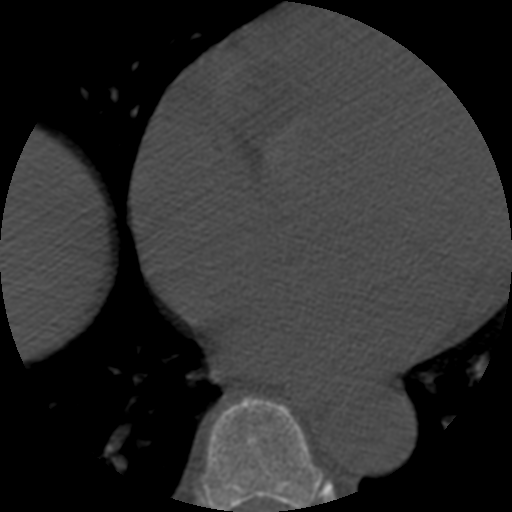
CT including the spine, one axial slice. Position 327 of 508 along the scan axis. Bone window (W 1800 / L 400 HU). 1.25 mm slice thickness. 512 × 512 image matrix, field of view 160 × 160 mm. Patient age 57 years. Case-level facts recorded for this patient, not image findings: primary cancer: prostate.
Annotated regions visible in this slice (semi-automatically segmented with operator editing):
- T7 vertebra: bounding box (x1, y1, x2, y2) in pixels: (202, 398, 326, 512)